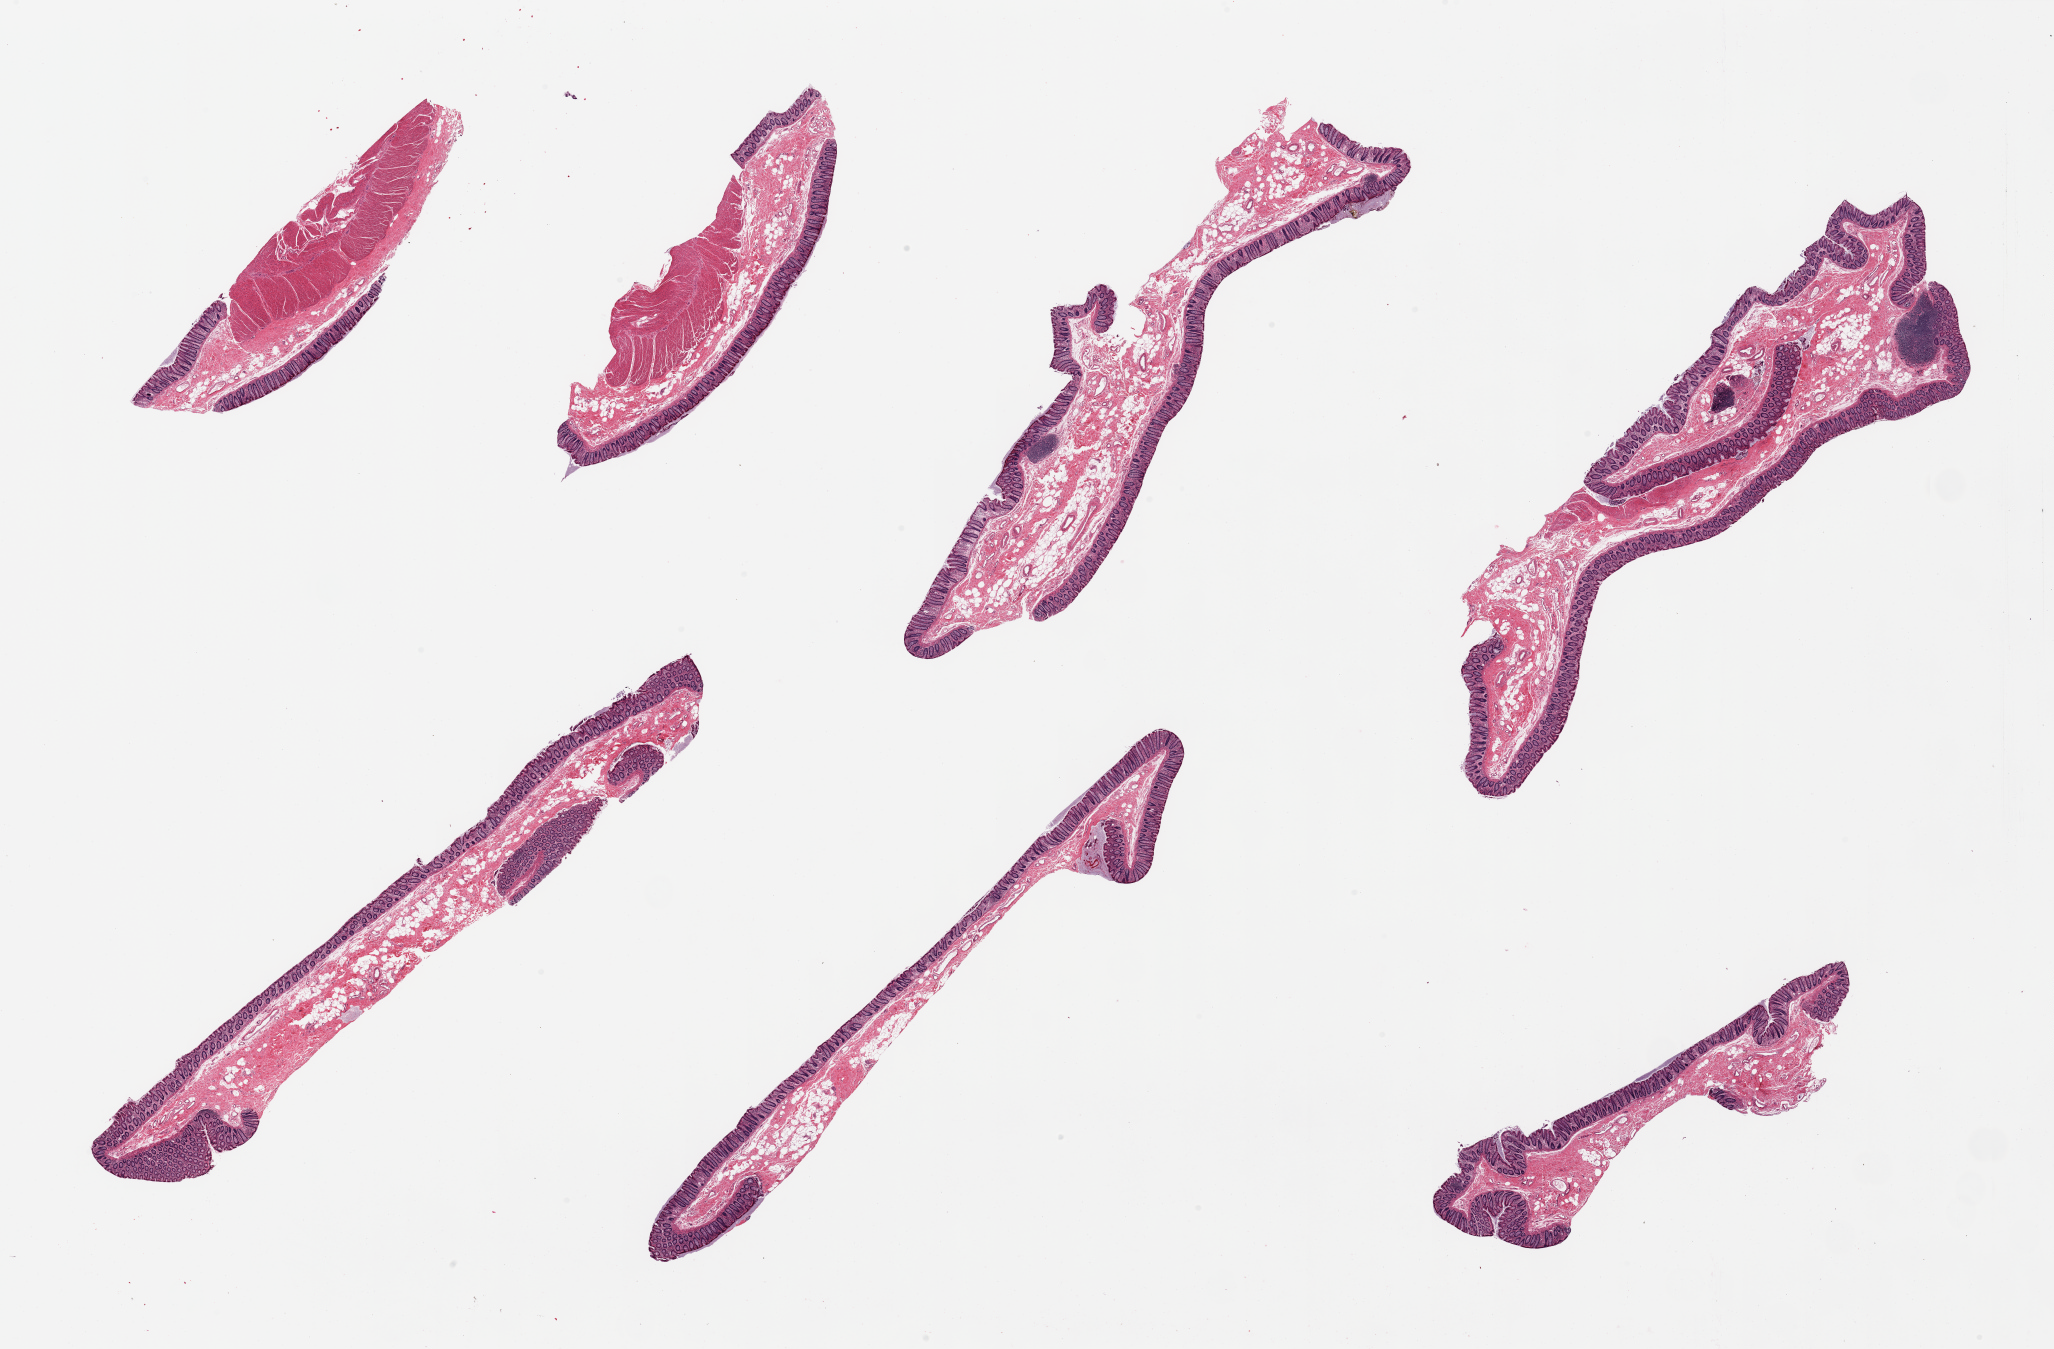
H&E whole-slide image, whole scanned area (about 32.5 x 21.3 mm) shown as a low-resolution overview. PAXgene-fixed, paraffin-embedded tissue. Sampled site (target tissue): transverse colon. Donor tissue sample.
Reviewer comment on this tissue sample: 7 pieces, mucosa well preserved, ~0.3mm.